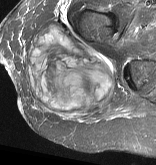
MRI of an extremity soft-tissue mass, one axial slice. Slice 26 of 57 in the series (ordered by position). STIR. MR volume resampled by the dataset authors to the PET/CT grid (not the native acquisition matrix). 3.27 mm slice thickness. 156 × 165 image matrix. Female patient. From the clinical record (not read from this slice): histological type: epithelioid sarcoma with vascular differentiation; site of the primary tumour: right buttock.
Outlined on this slice (expert contour drawn on MRI and transferred to this co-registered scan by the dataset authors):
- gross tumour volume (mass): bounding box (x1, y1, x2, y2) in pixels: (26, 26, 116, 118)